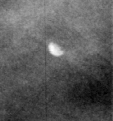
Region of interest cut from a scanned film mammogram (one marked finding), left breast, CC view, BI-RADS breast density category 3 (scale 1–4).
Calcifications, morphology lucent center; BI-RADS assessment category 2; benign without callback (not worked up further).